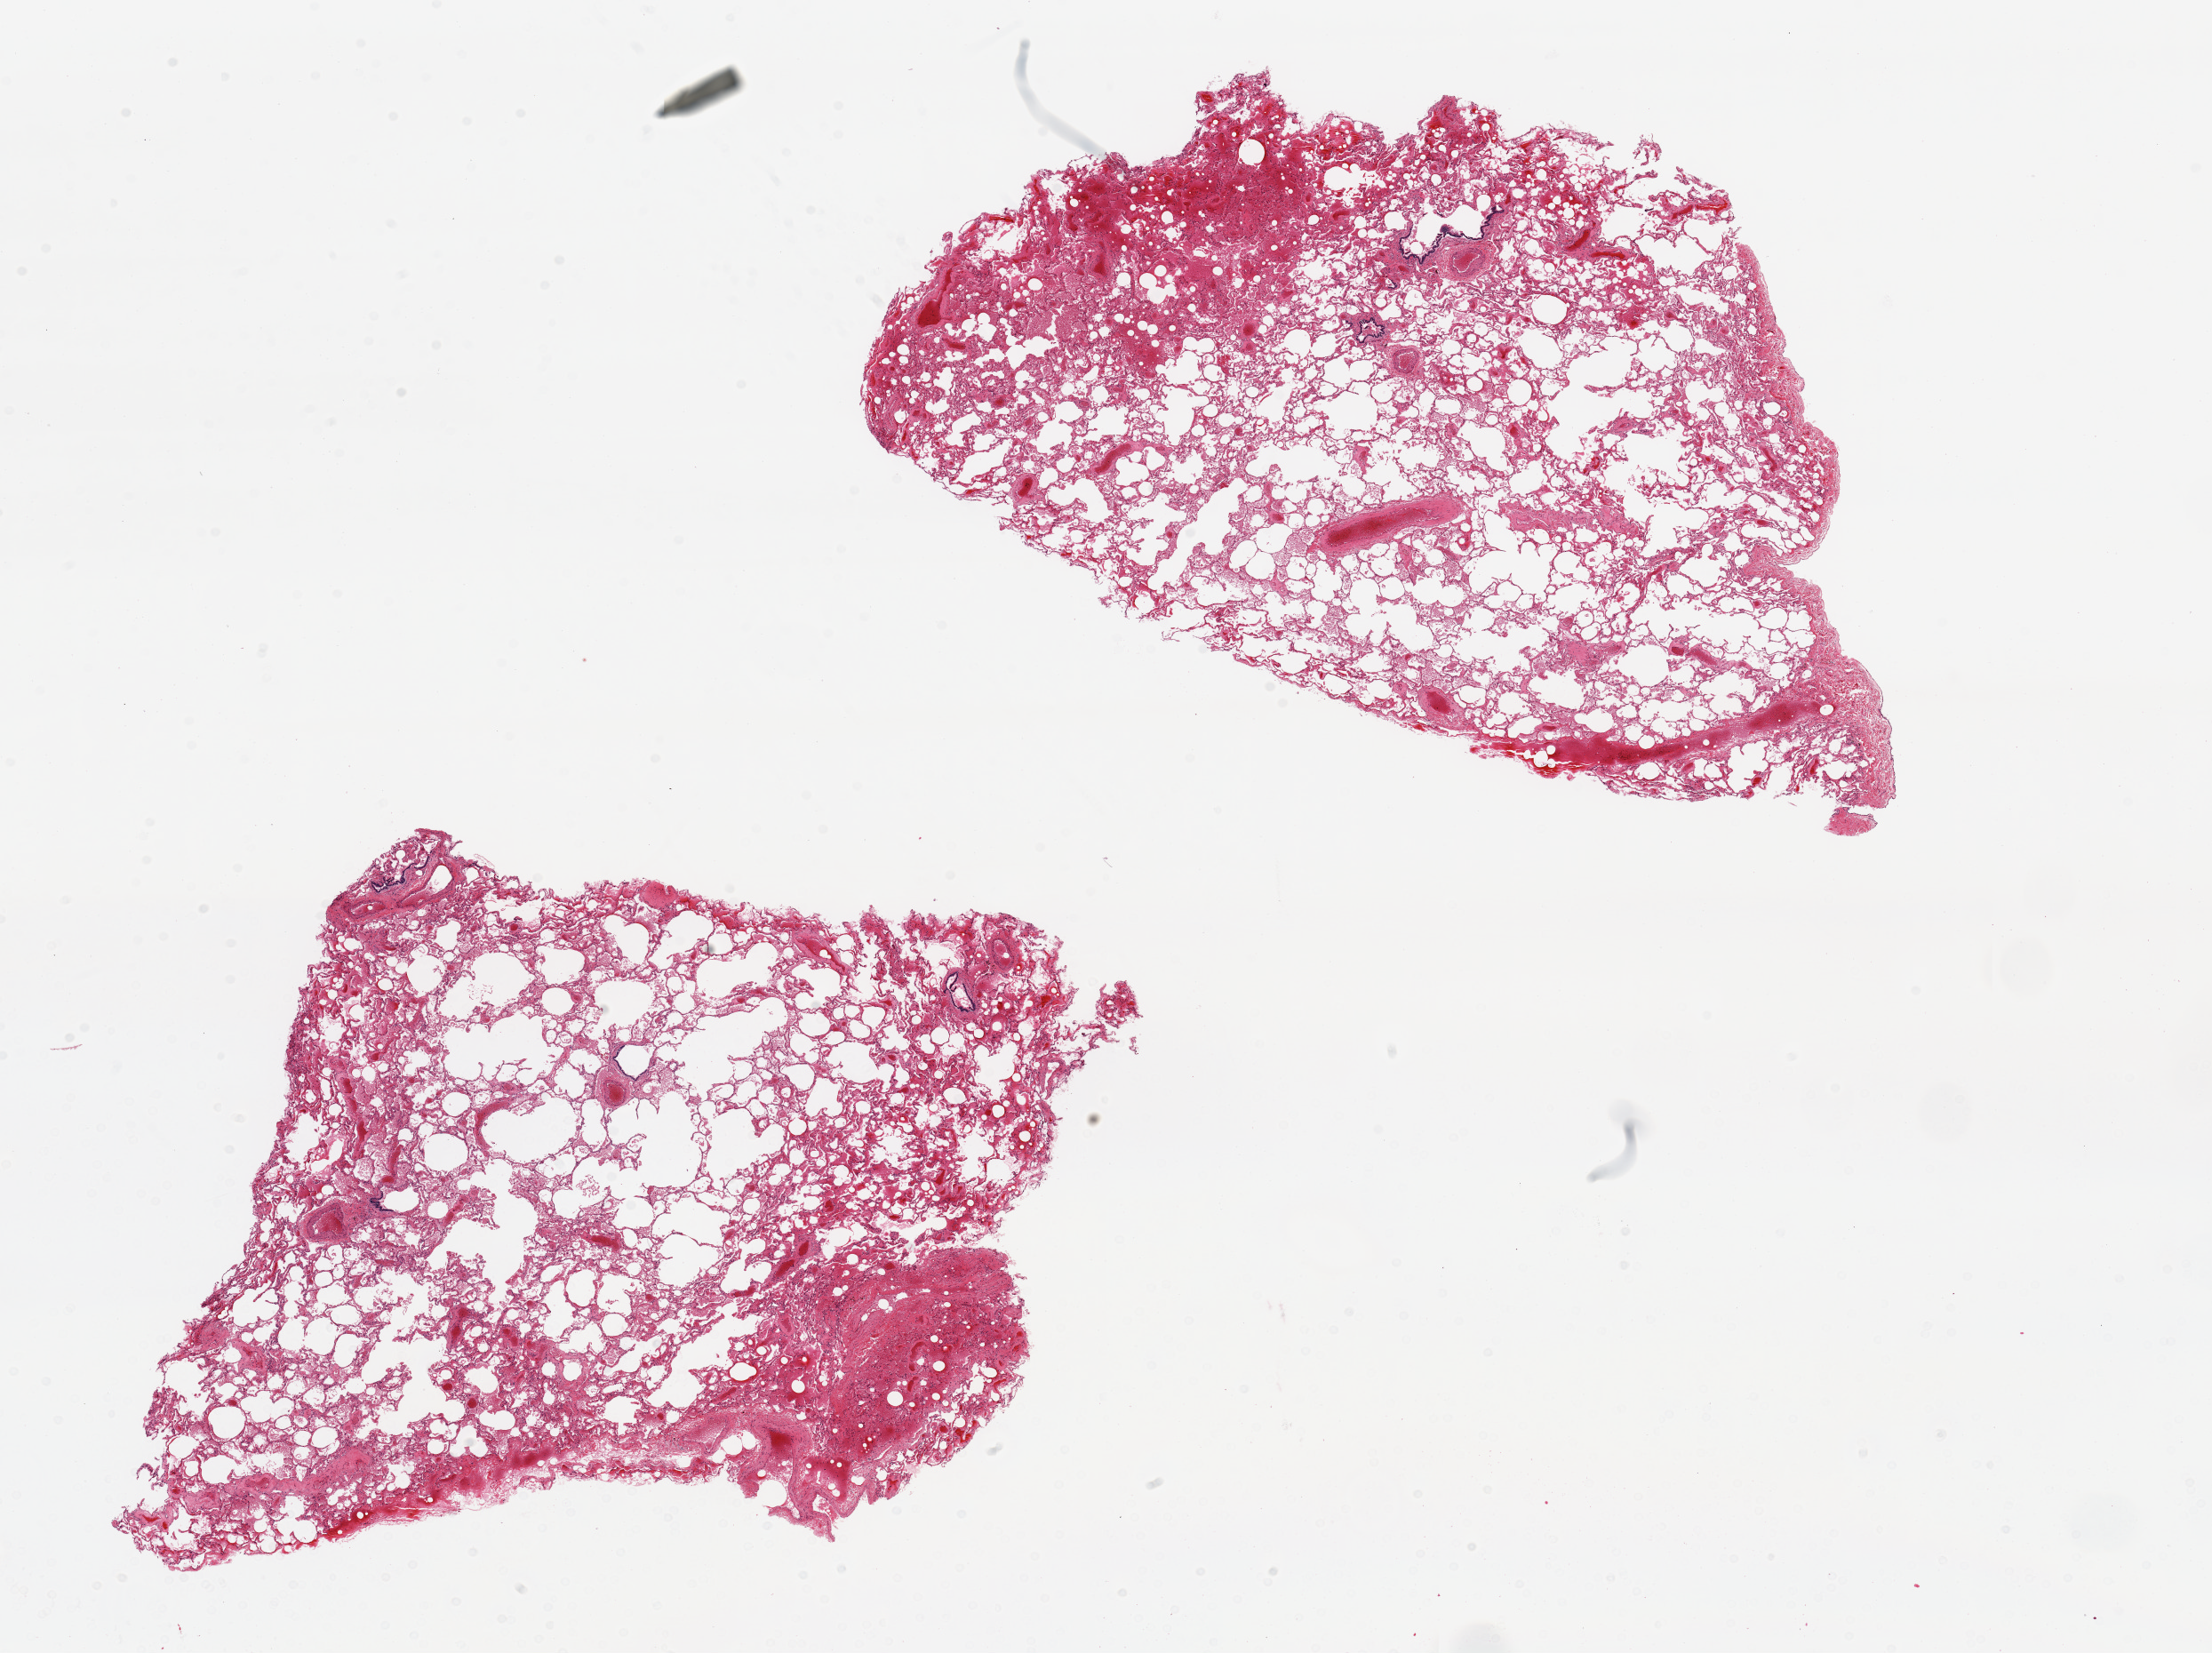
H&E whole-slide image, whole scanned area (about 19.7 x 14.7 mm, slide scanned at 20x) shown as a low-resolution overview; PAXgene-fixed paraffin-embedded (PFPE) section; sampled site (target tissue): lung; tissue donor sample. Donor: female.
Reviewer comment on this tissue sample: 2 pieces, 7x6 & 10x5 mm; focal hemorrhages.